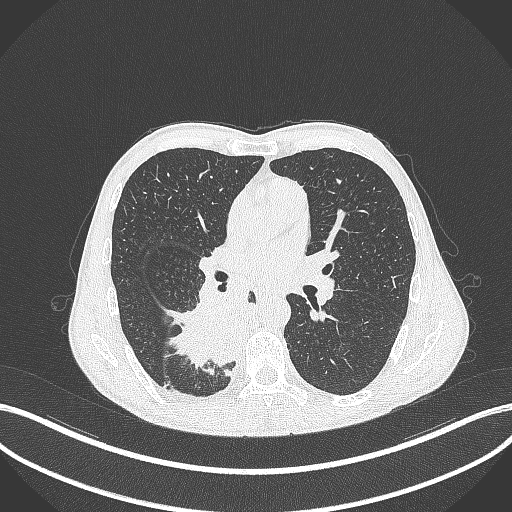
Chest CT, one axial slice. Slice 199 of 371 in the series (ordered by position). Reconstruction kernel B70f. 120 kVp. Lung window (W 1500 / L -600 HU). 1 mm slice thickness. 512 × 512 image matrix. Male patient, age 58 years. From the clinical record (not read from this slice): clinical TNM (as recorded): T3 N1 M1.
Annotated regions visible in this slice (rectangle marked by the reading radiologist):
- lung tumour (recorded histology: squamous cell carcinoma): bounding box <162,275,254,375> (left, top, right, bottom; pixels)